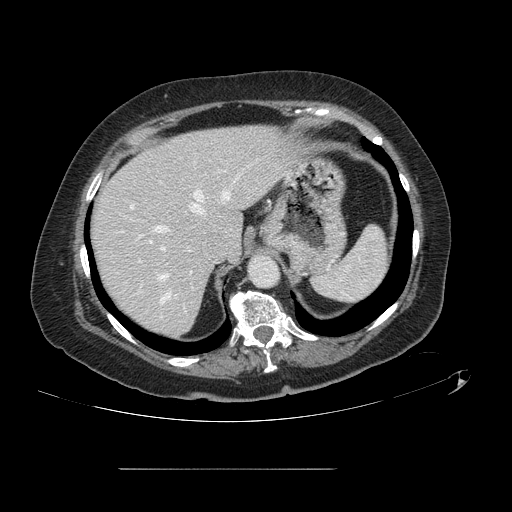
Contrast-enhanced abdominal CT, one axial slice. Slice 104 of 148 in the series (ordered by position). 120 kVp. Intravenous contrast given. Soft-tissue window (W 400 / L 40 HU). 512 × 512 image matrix, field of view 439 × 439 mm. Female patient, age 75 years. Case-level facts recorded for this patient, not image findings: diagnosis: colorectal cancer liver metastases, imaged before liver resection; multiple liver metastases: no; largest metastasis: 2.4 cm; disease in both lobes: no.
Structures marked on this image (expert manual segmentation):
- hepatic veins: box from (x=156, y=169) to (x=240, y=303) px
- liver: (x=91, y=126)–(x=290, y=337)
- planned liver remnant (the part of the liver to remain after resection): (x=91, y=126)–(x=291, y=337)
- portal vein (with intrahepatic branches): (x=131, y=205)–(x=165, y=250)